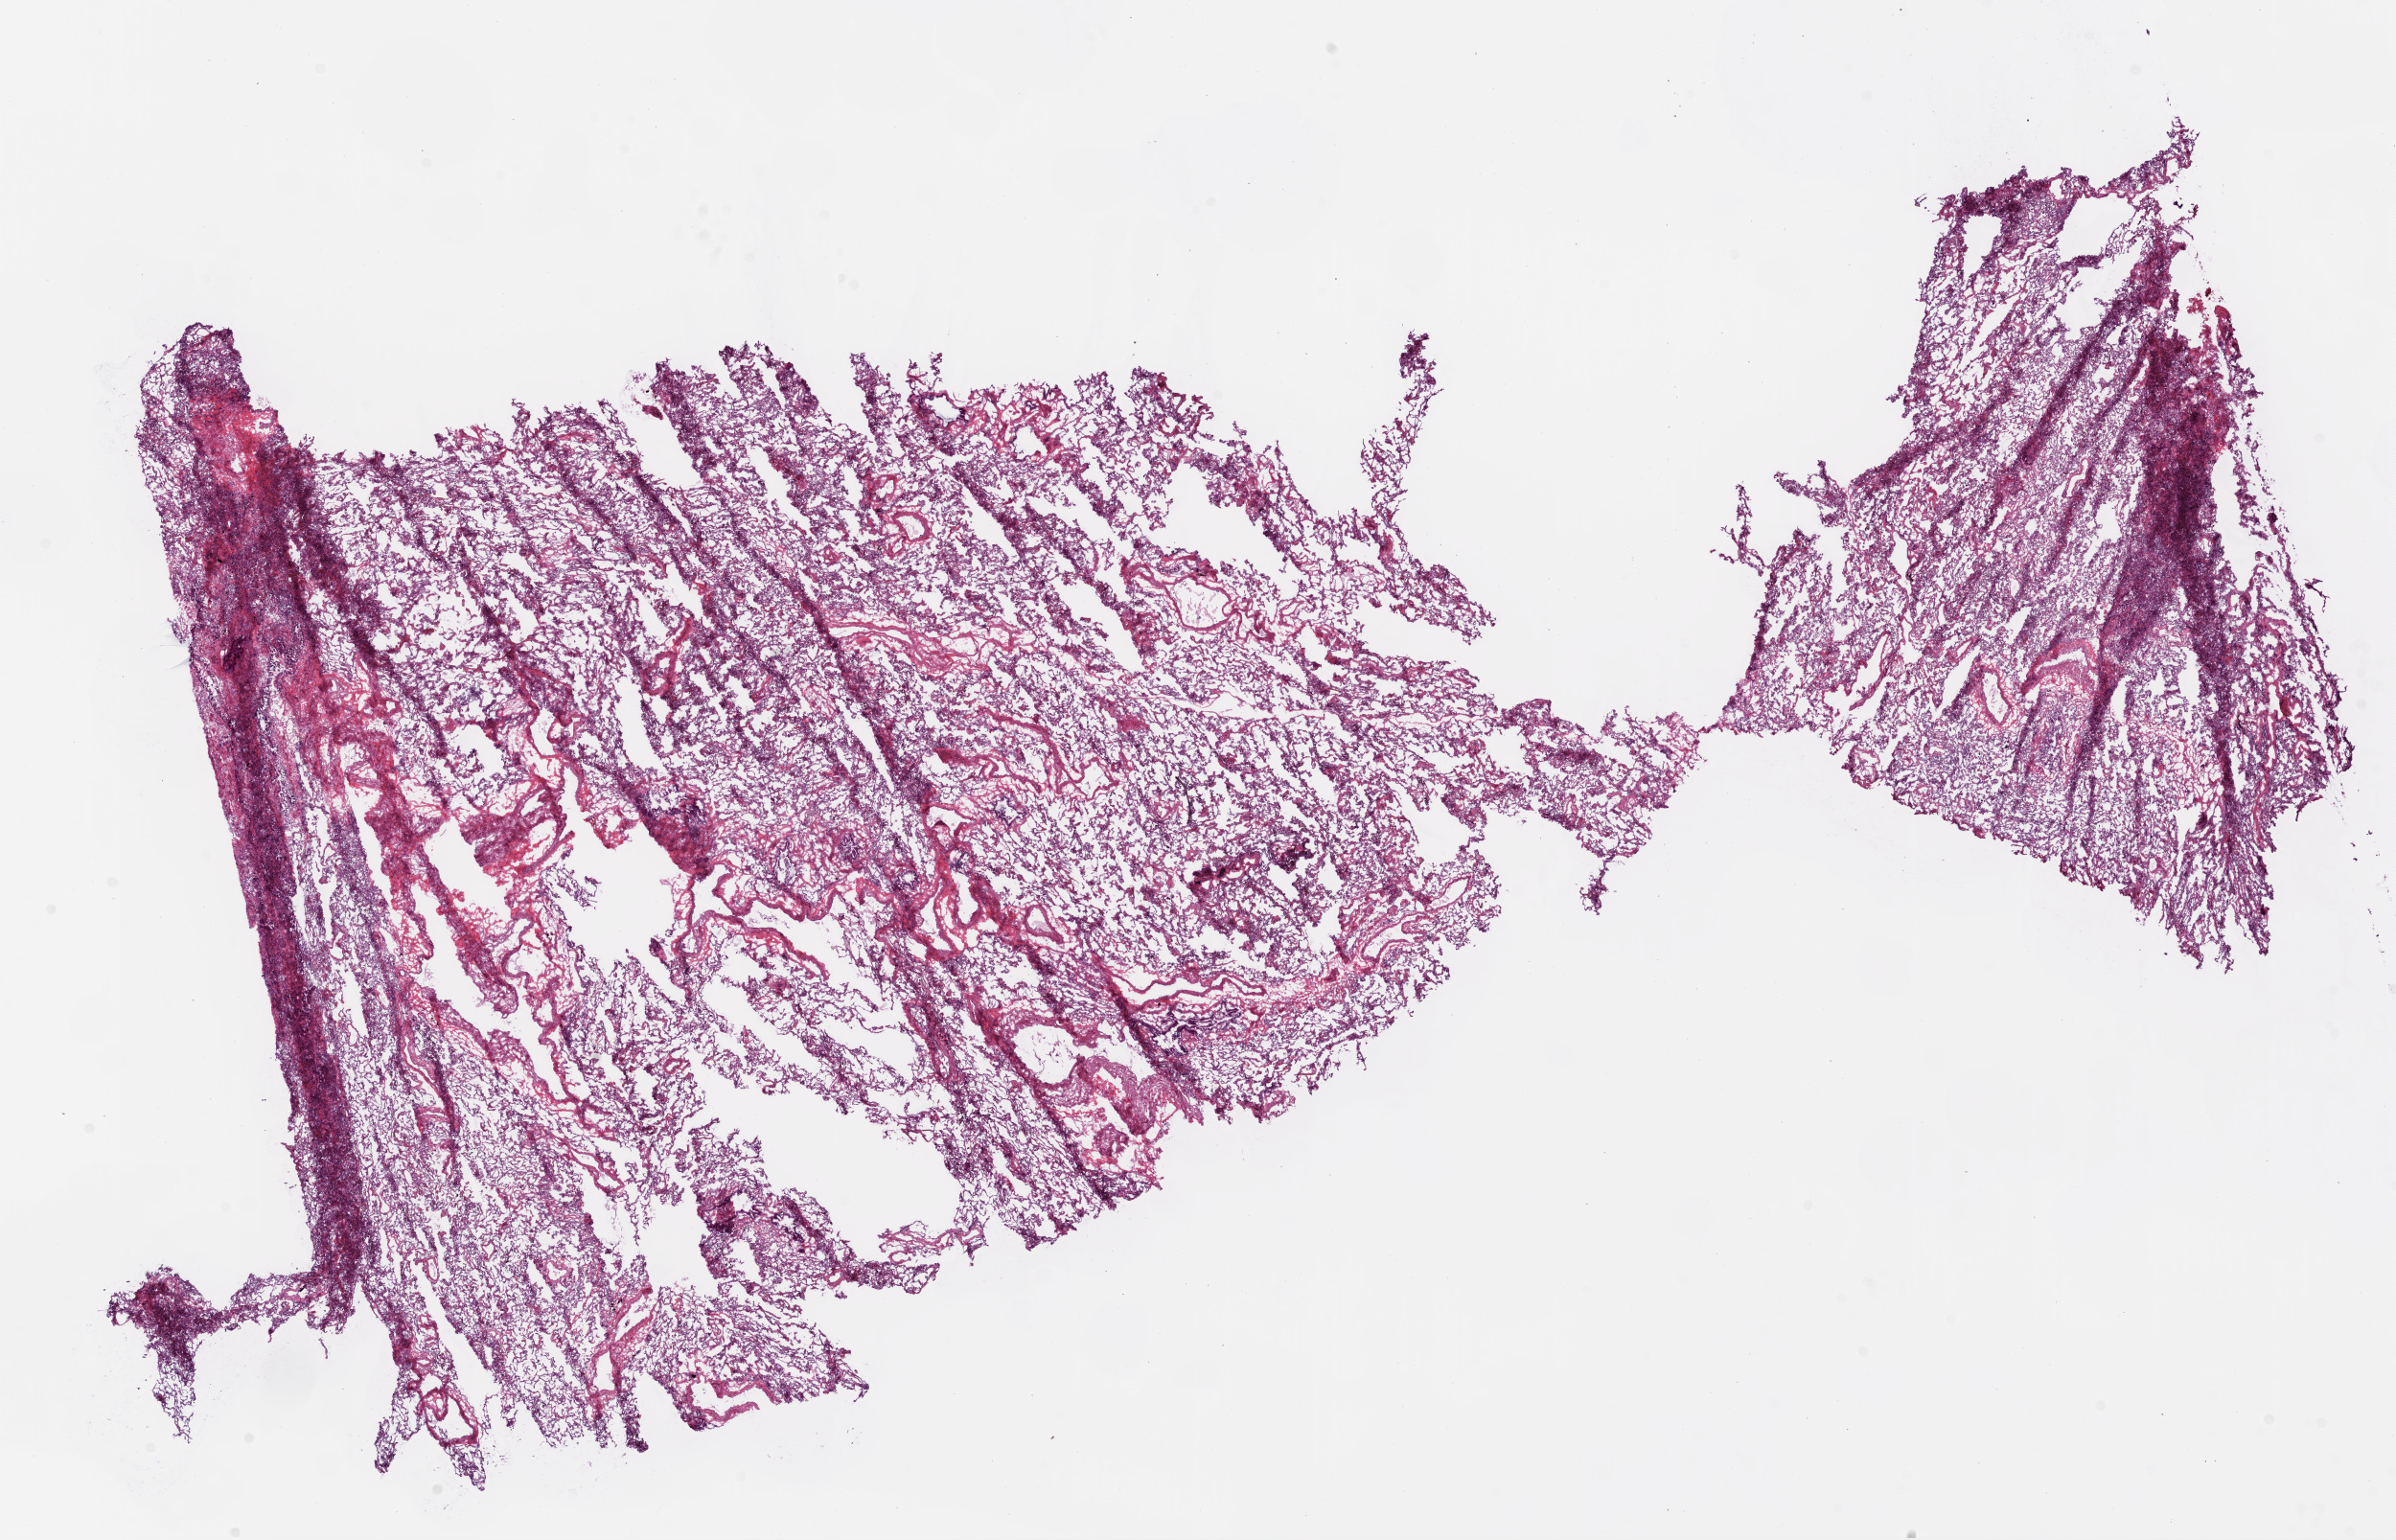
Digitized Hematoxylin and eosin (H&E) stained tissue section (whole slide) — low-resolution overview of the scanned area, about 20.1 x 12.9 mm (from a 20x scan), frozen section from the bottom of the tissue portion, sample: solid tissue normal (non-tumour tissue), lung. Patient: female, age at initial diagnosis 67 years.
This section: solid tissue normal (non-tumour) sample from the same patient. Patient diagnosis: Squamous cell carcinoma, NOS (upper lobe, lung).